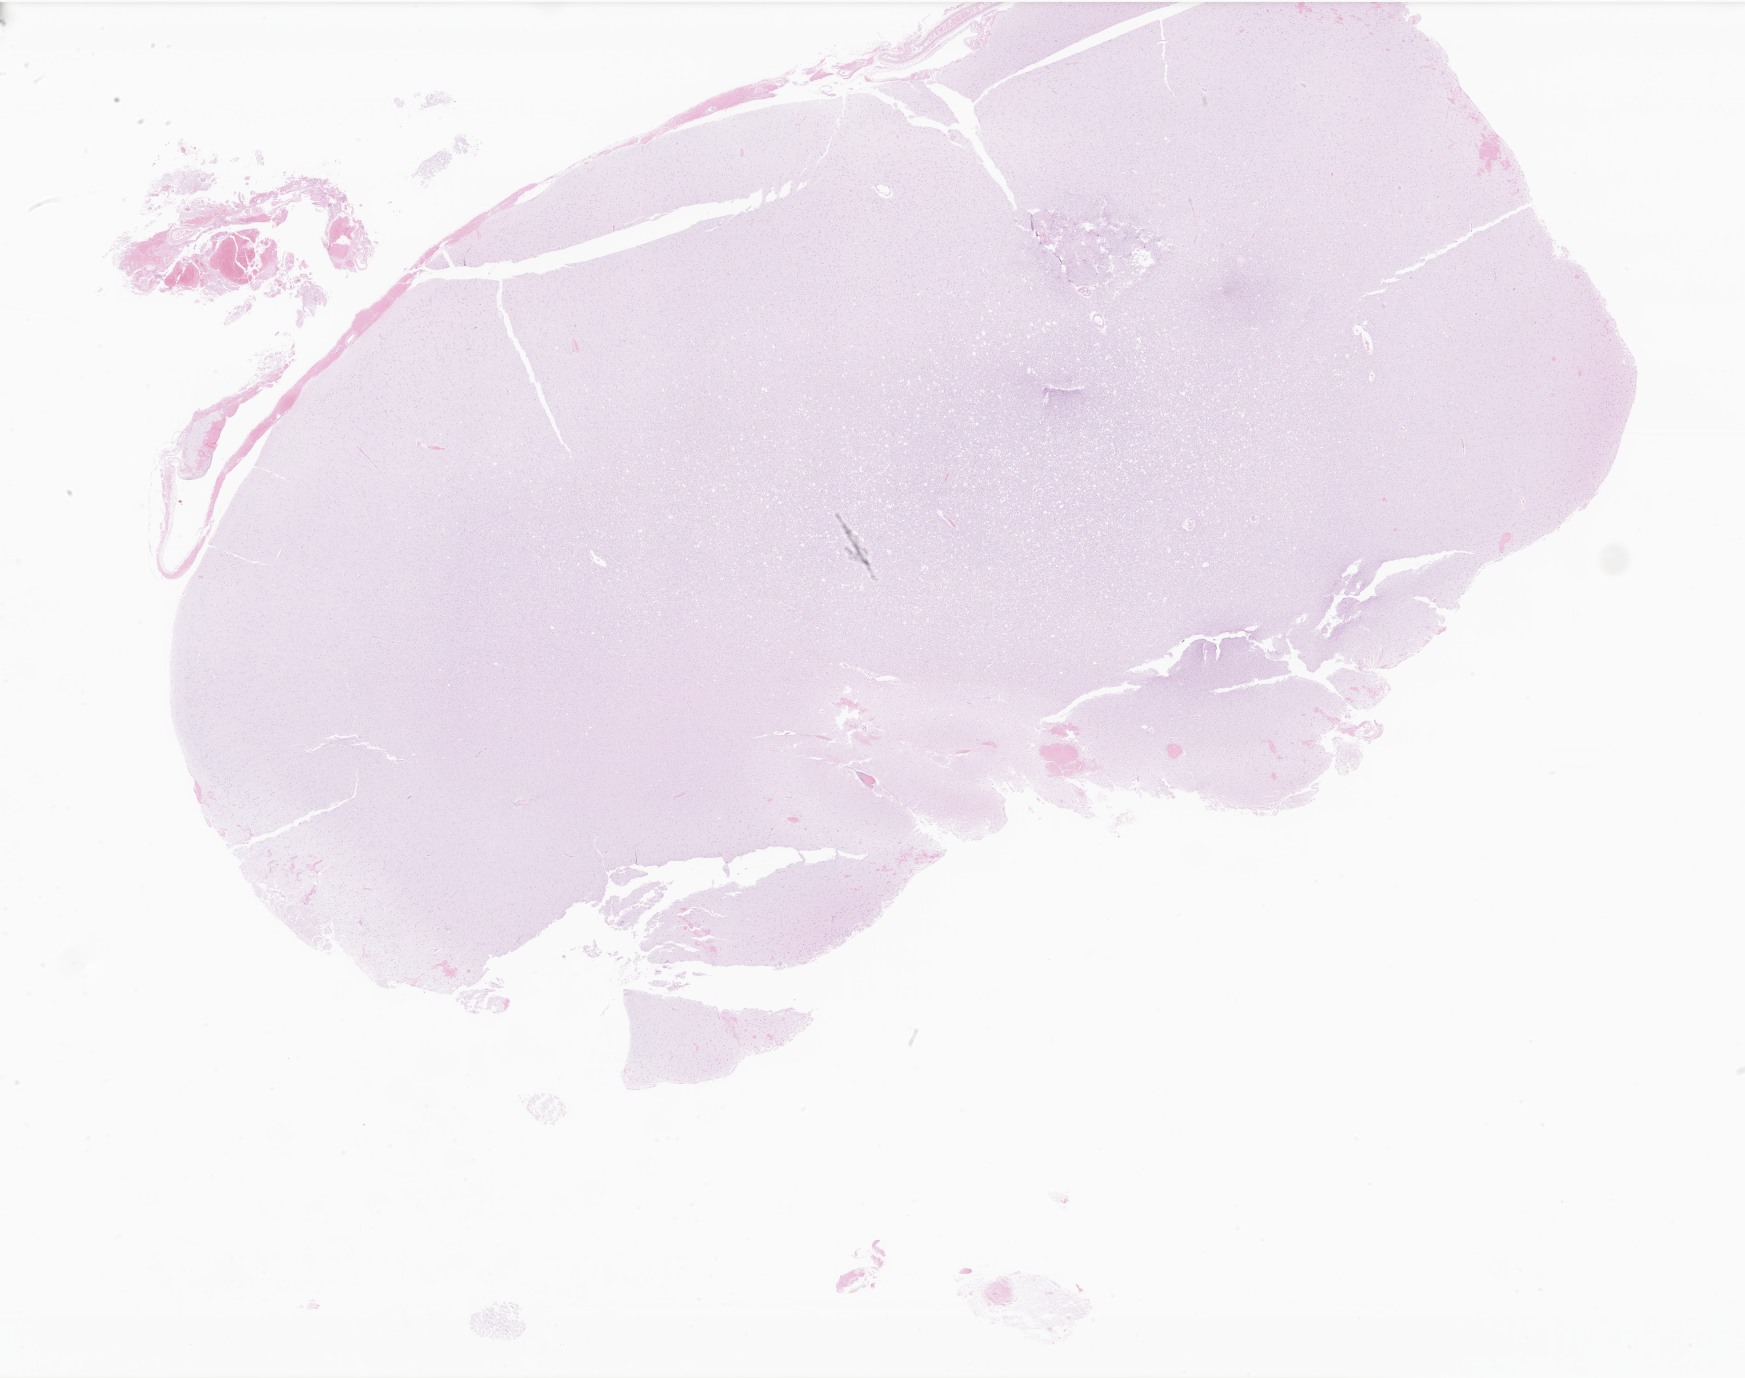
Whole-slide image, haematoxylin and eosin stain of tumor tissue from the parietal lobe — a low-resolution overview of the entire scanned area, about 29.4 x 23.2 mm. Formalin-fixed paraffin-embedded section. Patient female; age 240 months (20 years).
- recorded diagnosis: Astrocytoma, NOS